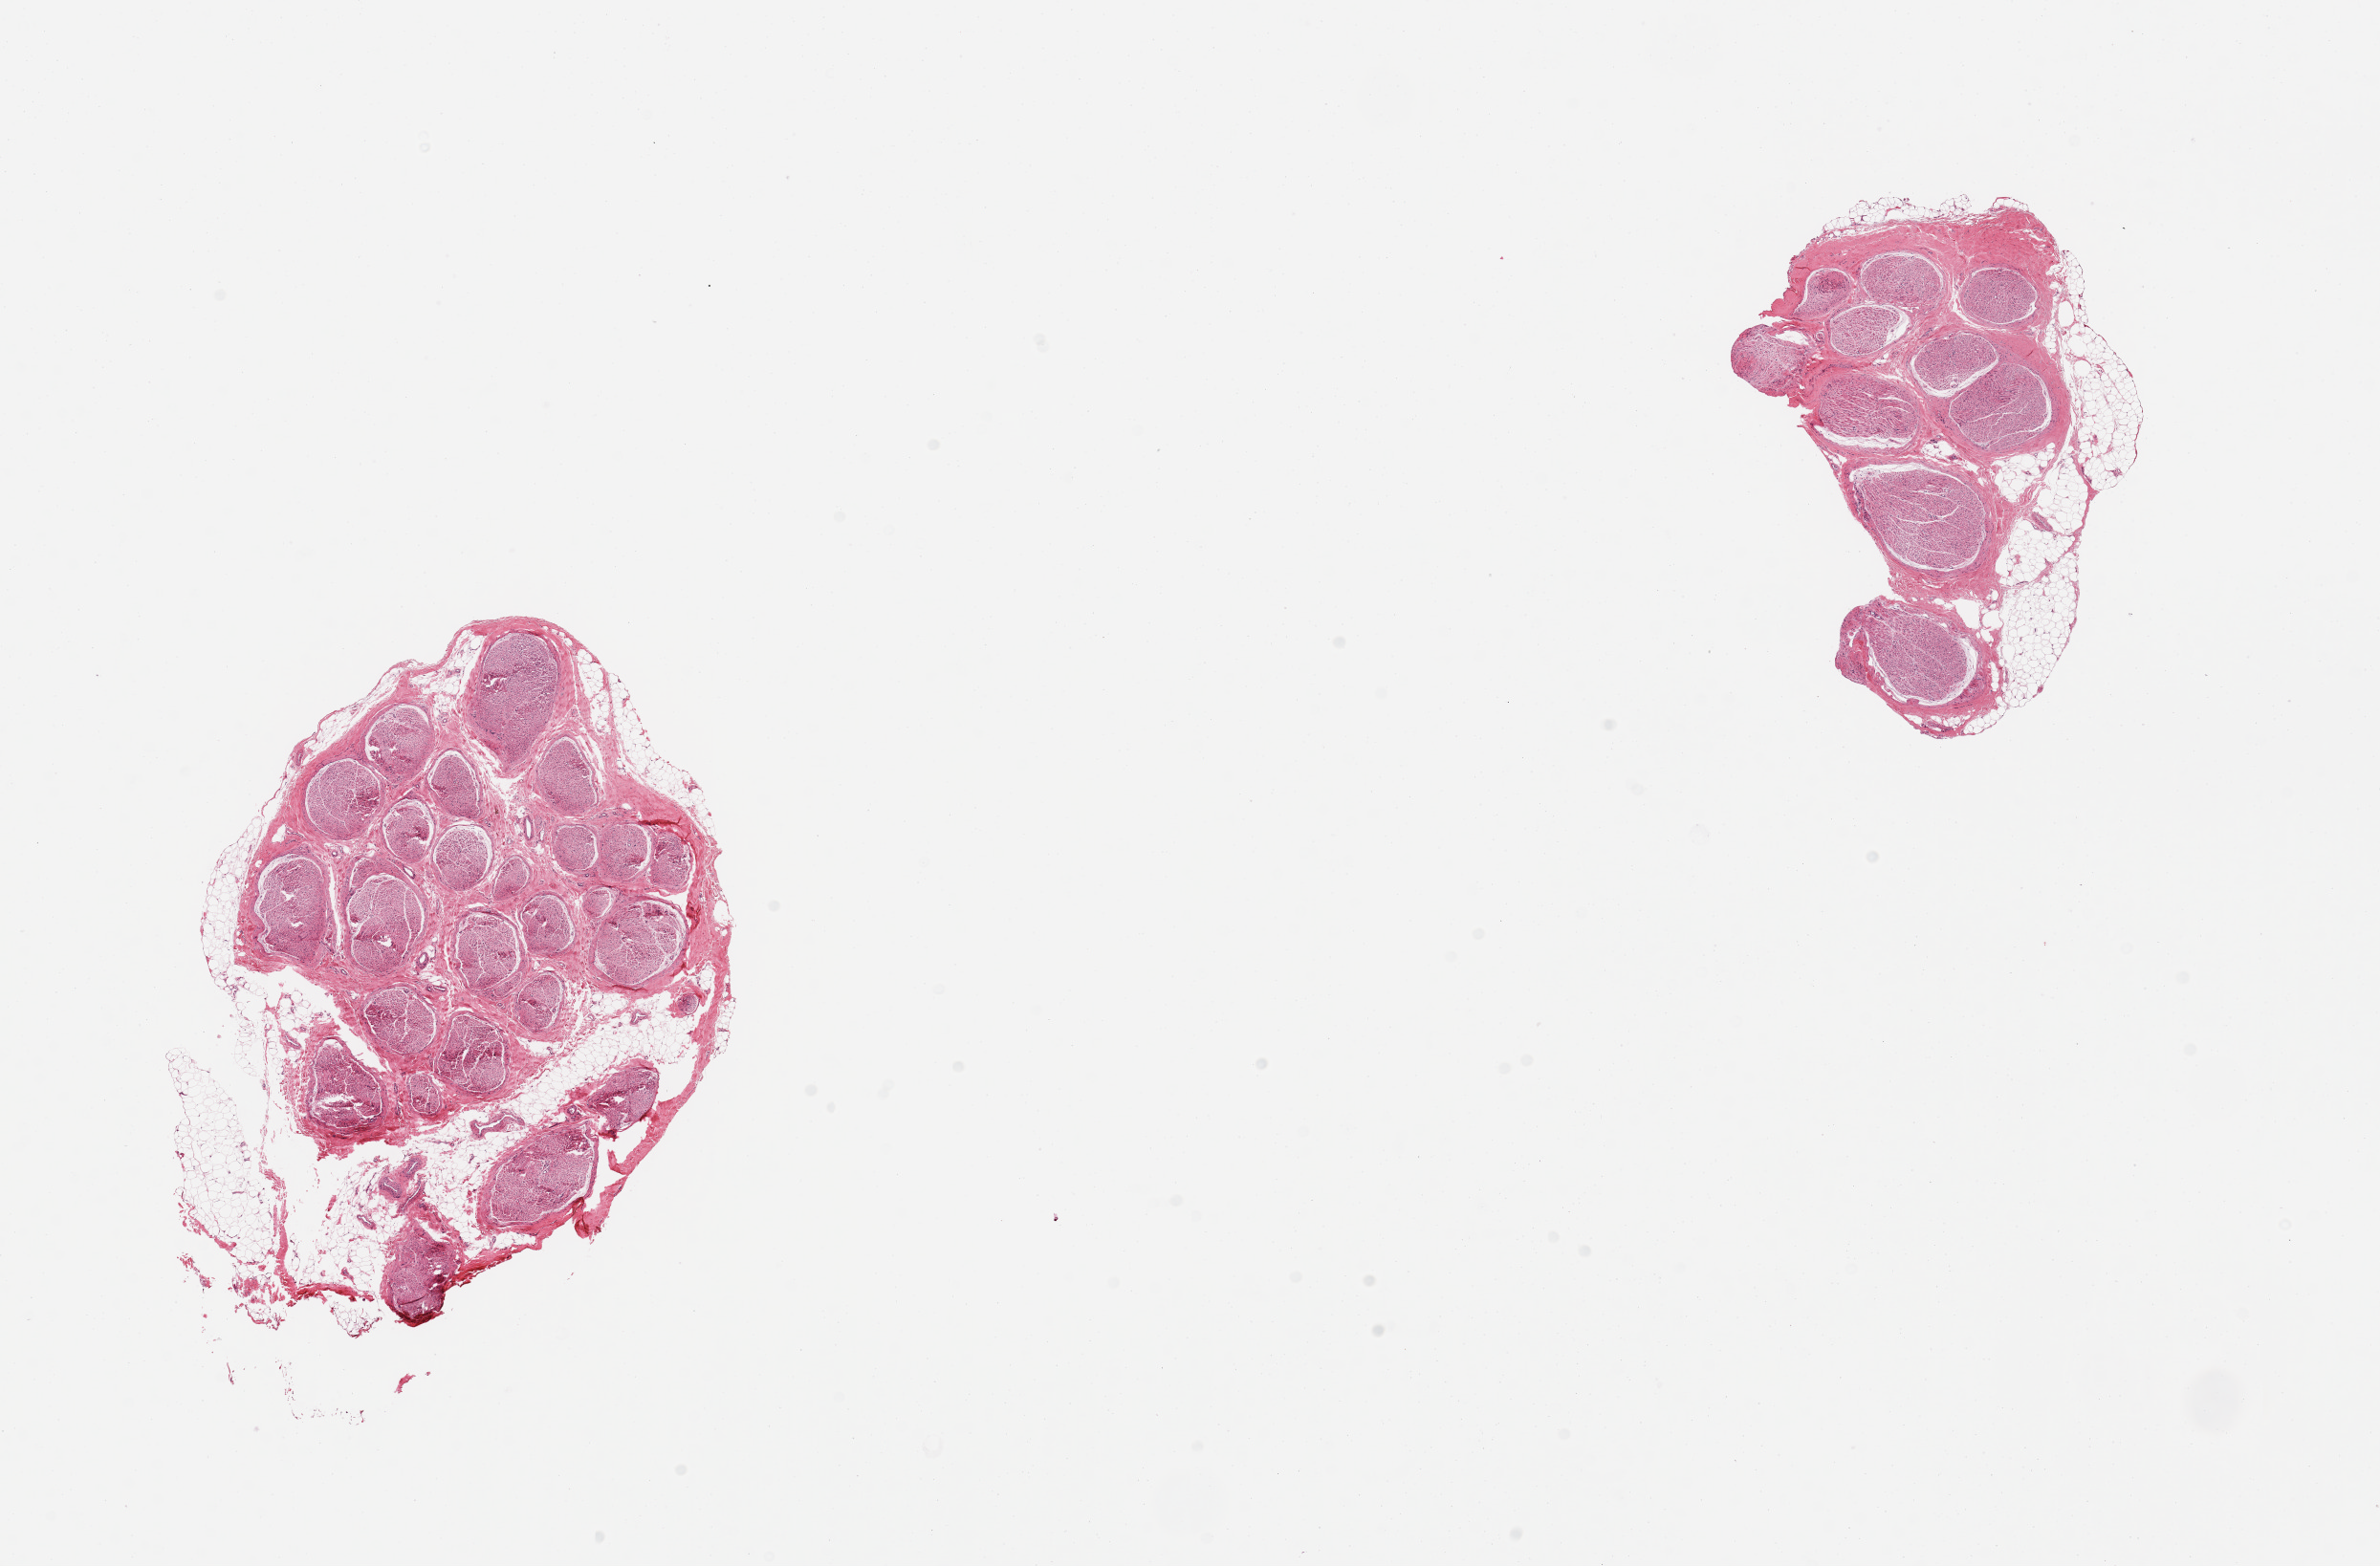
Whole-slide image, haematoxylin and eosin stain, brightfield, low-resolution overview of the scanned area, about 19.7 x 13.0 mm, PAXgene-fixed paraffin-embedded (PFPE) section, sampled site (target tissue): tibial nerve, tissue donor sample. Donor sex: male.
Review note (as recorded): 2 pieces, focally adherent fat up to ~0.5mm.